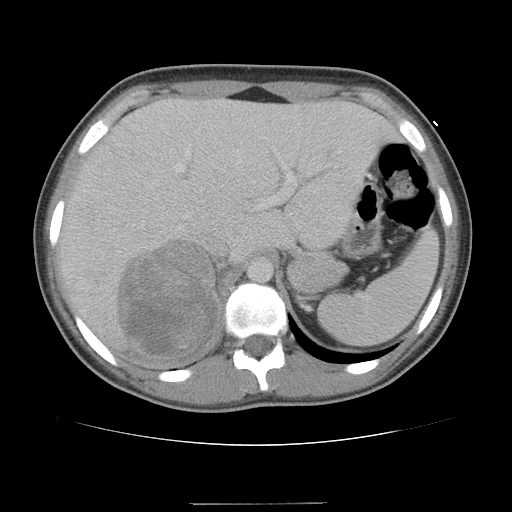
Contrast-enhanced abdominal CT, one axial slice. Position 78 of 100 along the scan axis. 120 kVp. Intravenous contrast given. Soft-tissue window (W 400 / L 40 HU). 5 mm slice thickness. 512 × 512 image matrix, field of view 360 × 360 mm. Patient: female, 21 years. Case-level facts recorded for this patient, not image findings: diagnosis: adrenocortical carcinoma; tumour side: right adrenal; tumour size at pathology: 15.5 cm; Ki-67 index: 26 %; stage (as recorded): 3.
Annotated regions visible in this slice (semi-automatic segmentation, software-assisted and operator-edited):
- mass: bounding box (x1, y1, x2, y2) in pixels: (118, 240, 216, 356)